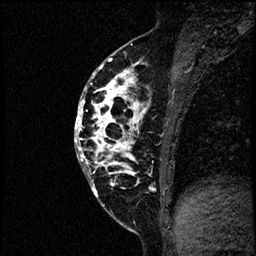
Breast MRI (dynamic contrast-enhanced), one sagittal slice; position 29 of 60 along the scan axis; dynamic contrast-enhanced study with each time point stored as its own series, time point 2 of 4 at this slice position (early post-contrast, ordered by acquisition time); 1.5 T; TE 4.2 ms, TR 17.6 ms; 2 mm slice thickness; 256 × 256 image matrix, field of view 200 × 200 mm. Patient: female, 40 years. From the clinical record (not read from this slice): setting: breast cancer imaged before/during neoadjuvant chemotherapy; receptor status: HER2-positive.
Outlined on this slice (semi-automatically segmented with operator editing):
- analysis volume of interest (the breast-tissue region the enhancement analysis was run in; not a lesion): bounding box (x1, y1, x2, y2) in pixels: (76, 56, 197, 205)
- tumour enhancement mask (voxels above the 100 % enhancement threshold inside the analysis volume of interest): (76, 58, 155, 194)